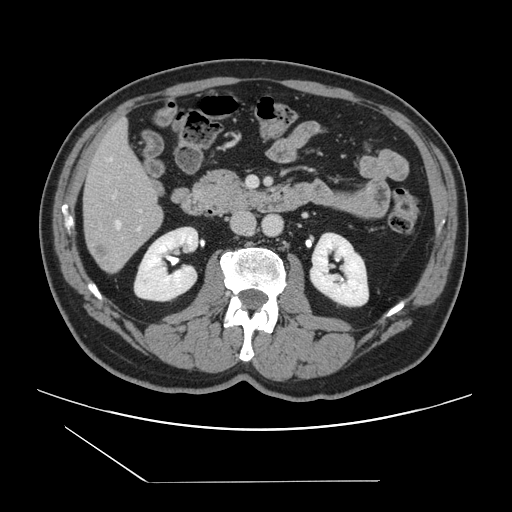
Contrast-enhanced abdominal CT, one axial slice. Slice 48 of 157 in the series (ordered by position). 120 kVp. Intravenous contrast given. Soft-tissue window (W 400 / L 40 HU). 512 × 512 image matrix. Male patient, age 61 years. Case-level facts recorded for this patient, not image findings: diagnosis: colorectal cancer liver metastases, imaged before liver resection.
Structures marked on this image (outlined manually by an expert reader):
- hepatic veins: bounding box [x1, y1, x2, y2] px = [109, 158, 121, 229]
- liver: [84, 123, 162, 272]
- planned liver remnant (the part of the liver to remain after resection): [84, 123, 159, 218]
- portal vein (with intrahepatic branches): [113, 196, 141, 230]
- liver metastasis: [95, 245, 104, 261]